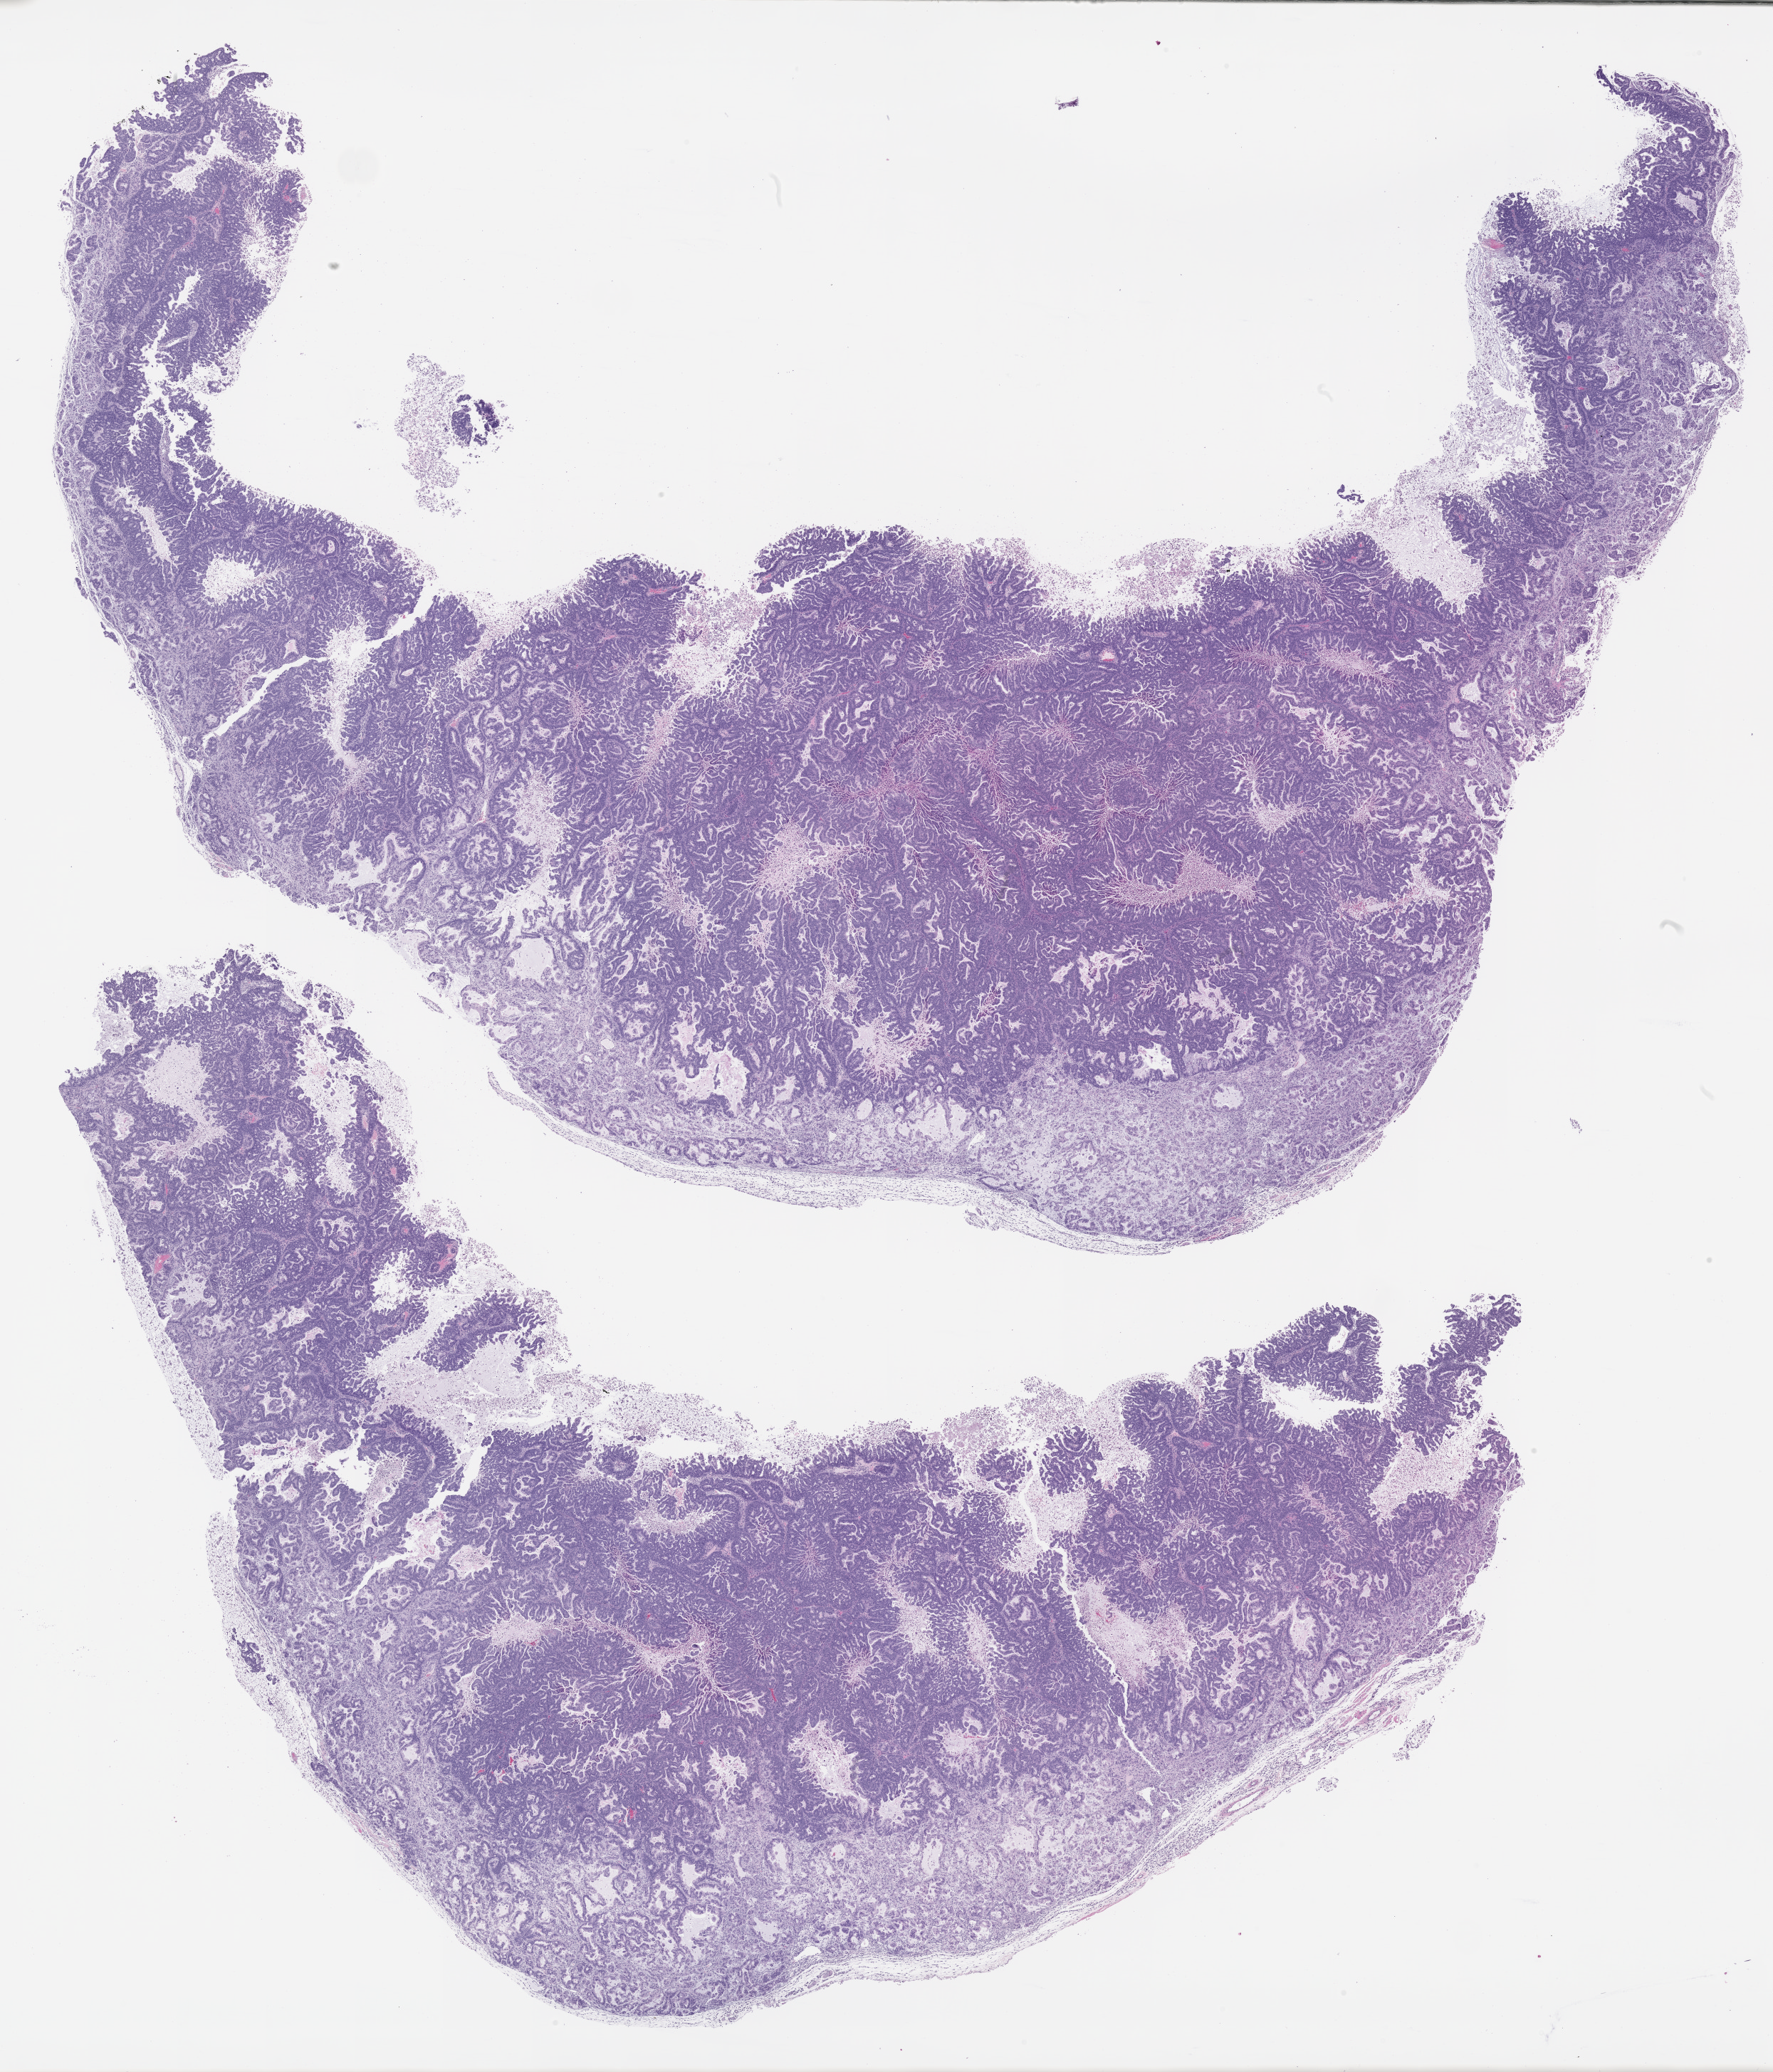
H&E whole-slide image of a patient-derived xenograft (PDX) tumor grown in a mouse, passage 1 — a low-resolution overview of the entire scanned area, about 20.0 x 23.4 mm; formalin-fixed paraffin-embedded section; originating tumor site category: pancreas.
Originating patient diagnosis: Pancreatic Adenocarcinoma.